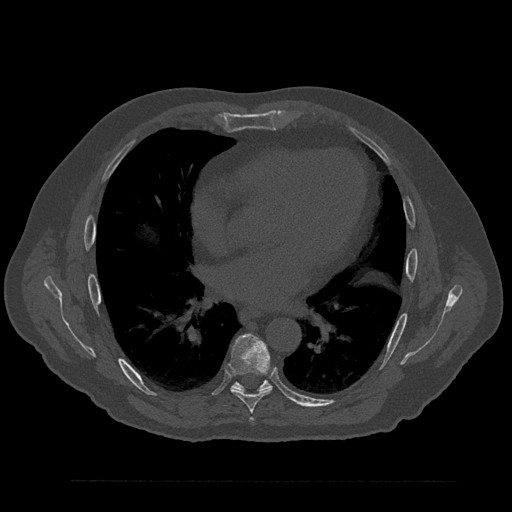
CT including the spine, one axial slice. Position 489 of 797 along the scan axis. Reconstruction kernel Br40s/3. 120 kVp. Bone window (W 1800 / L 400 HU). 0.5 mm slice thickness. 512 × 512 image matrix, field of view 430 × 430 mm. Male patient, age 61 years. From the clinical record (not read from this slice): primary cancer: prostate.
Annotated regions visible in this slice (semi-automatically segmented with operator editing):
- T6 vertebra: box from (x=250, y=418) to (x=253, y=421) px
- T7 vertebra: (x=229, y=335)–(x=272, y=413)
- T8 vertebra: (x=232, y=380)–(x=272, y=392)